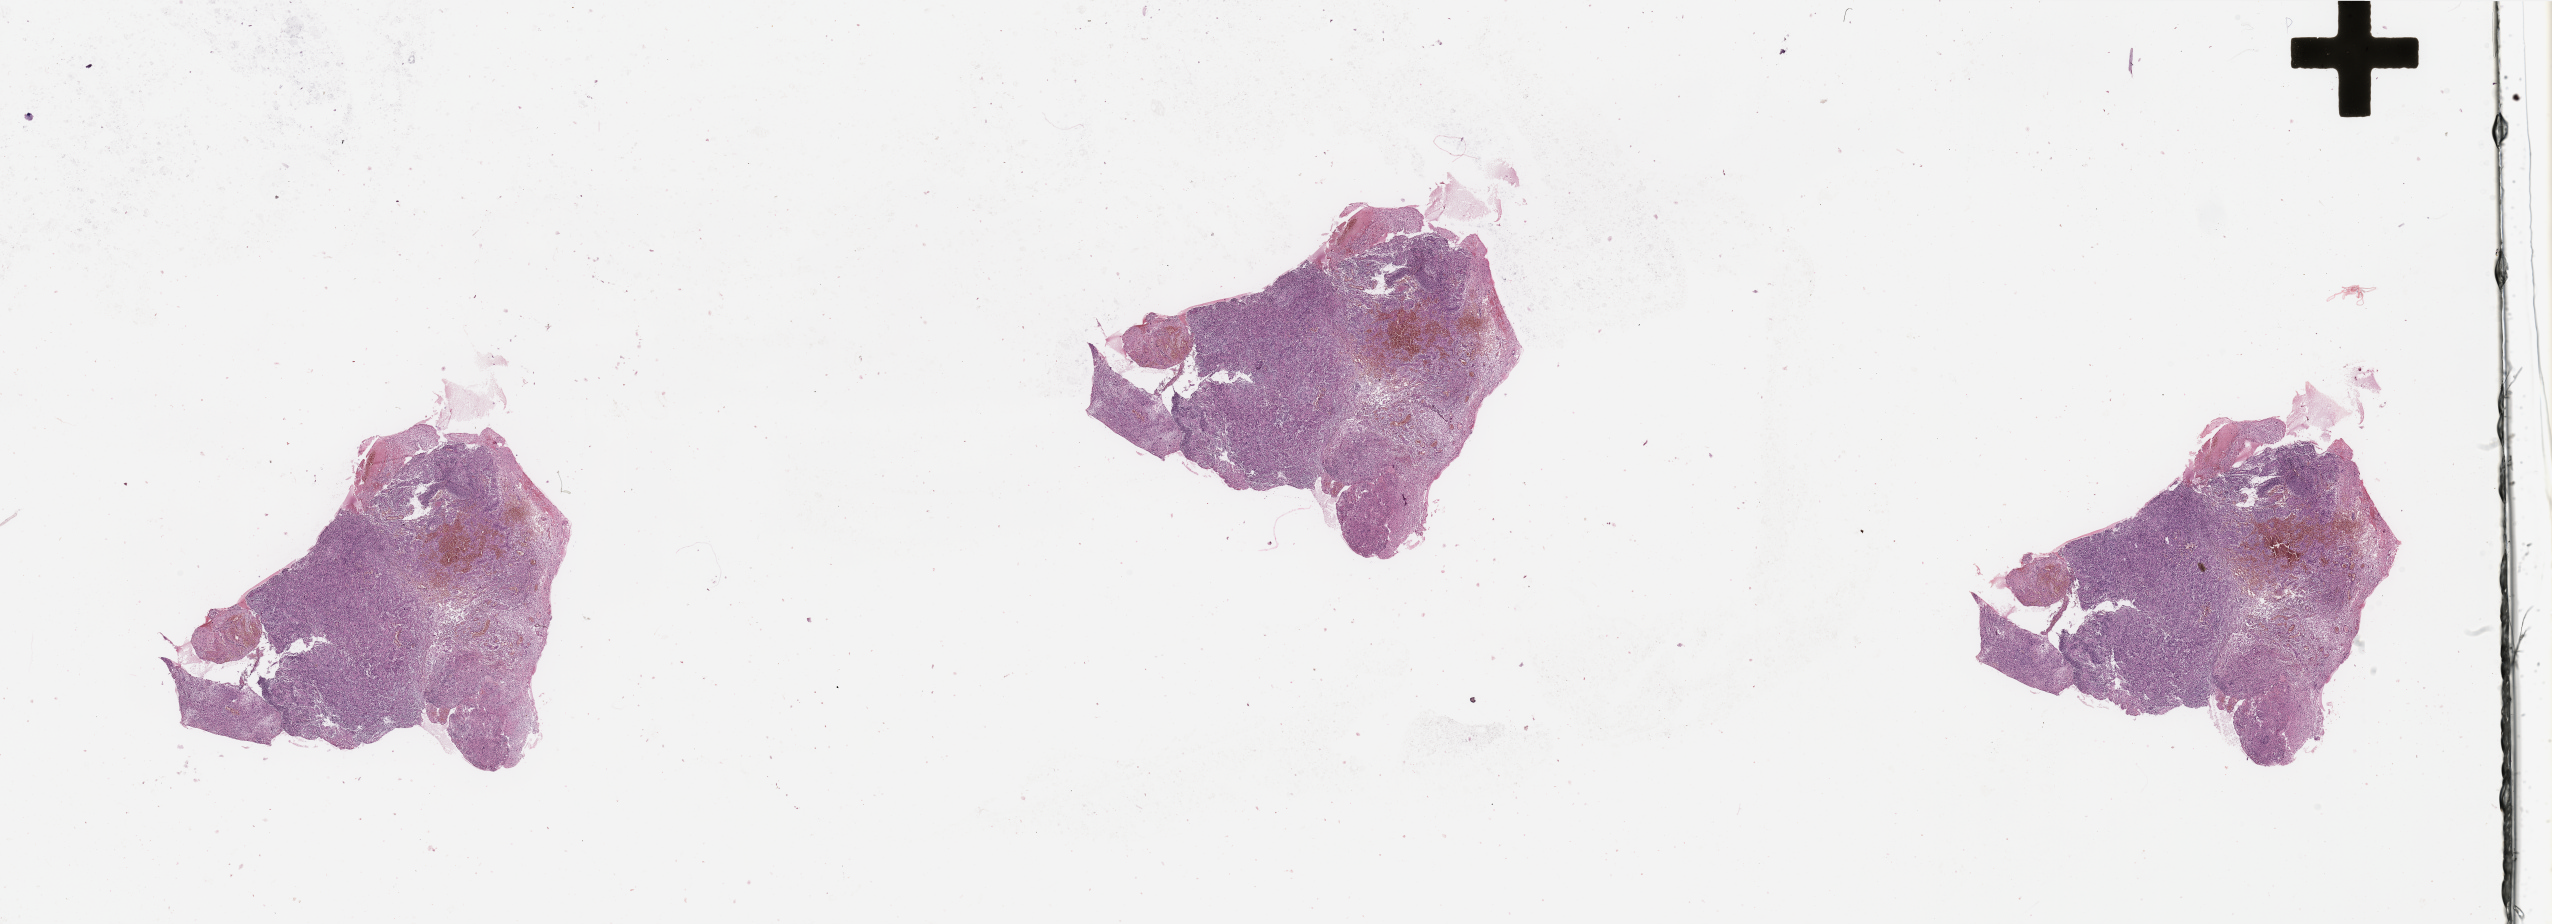
Whole-slide histology image, H&E — a low-resolution overview of the entire scanned area, about 40.4 x 14.6 mm; tumour tissue sample, sampled site: brain. Female, 58 y/o. Slide review estimates, as recorded: tumour nuclei 65%, necrosis 5%.
Diagnosis: Glioblastoma.